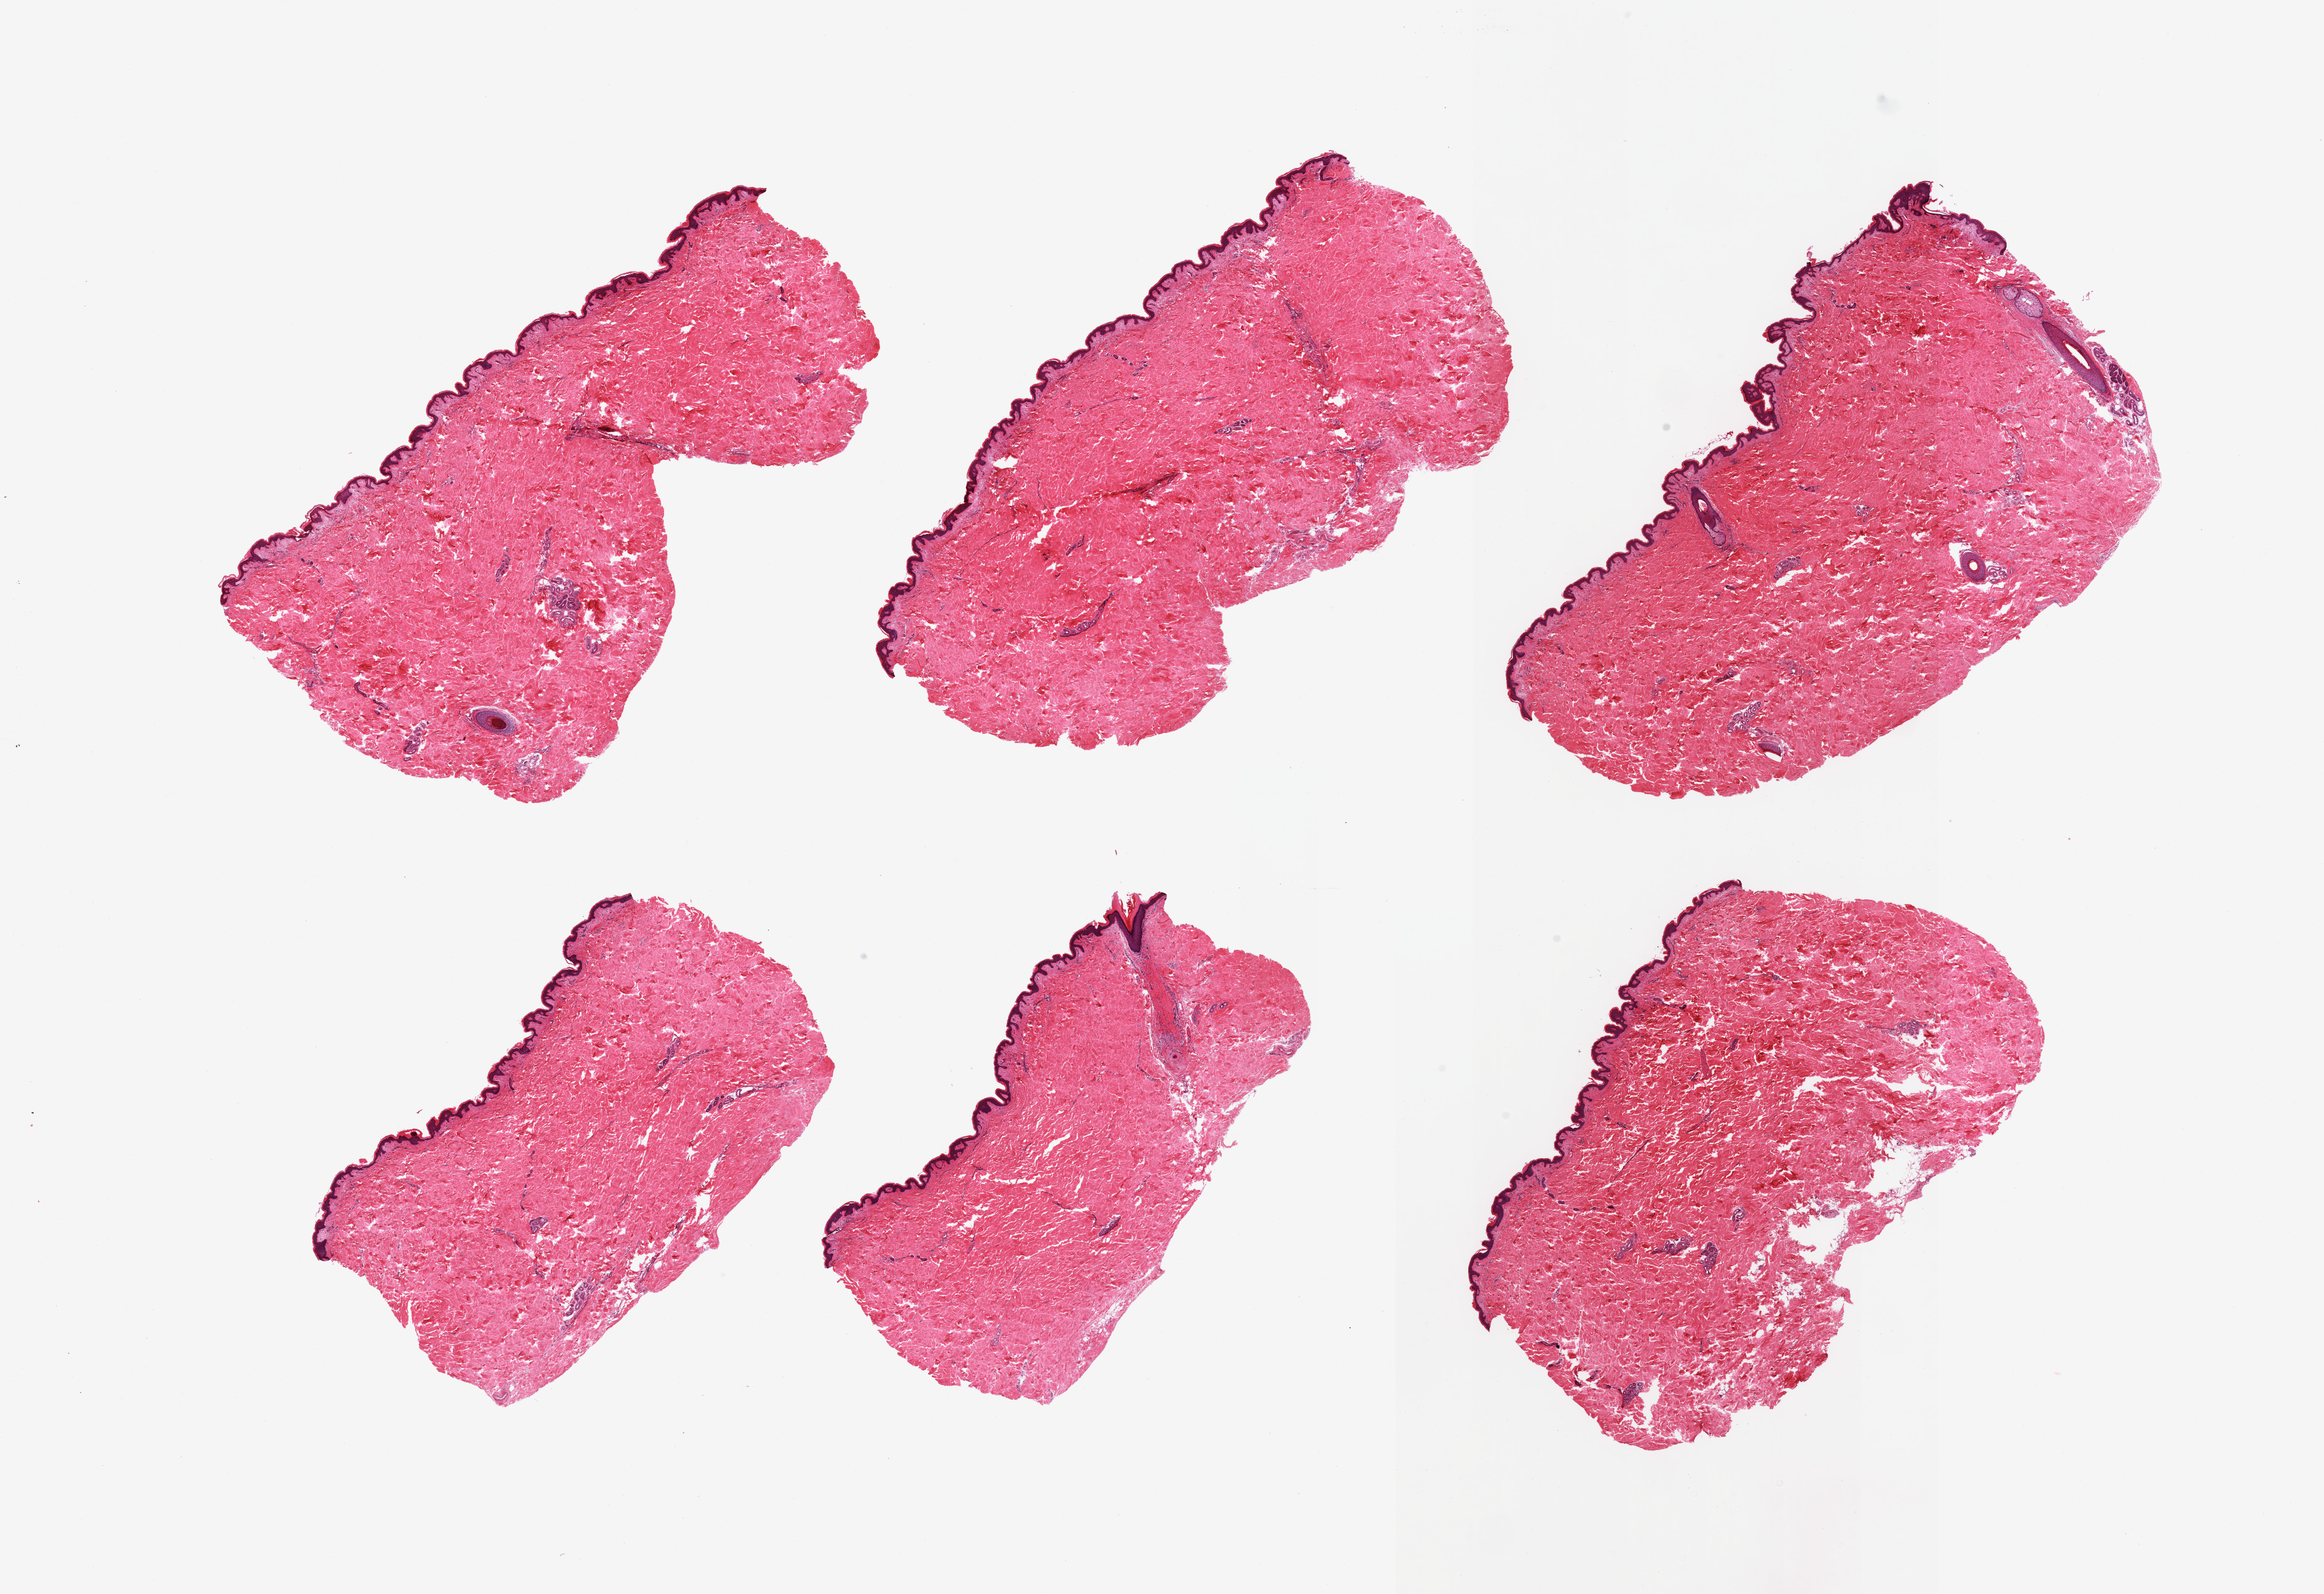
Haematoxylin and eosin whole-slide image, shown as a low-resolution overview of the whole scanned area (about 29.5 x 20.3 mm), PAXgene-fixed paraffin-embedded (PFPE) section, sampled site (target tissue): skin of suprapubic region, donor tissue sample. Donor sex: male.
Pathologist's review note for this sample: 6 pieces; insignificant periadnexal fat.